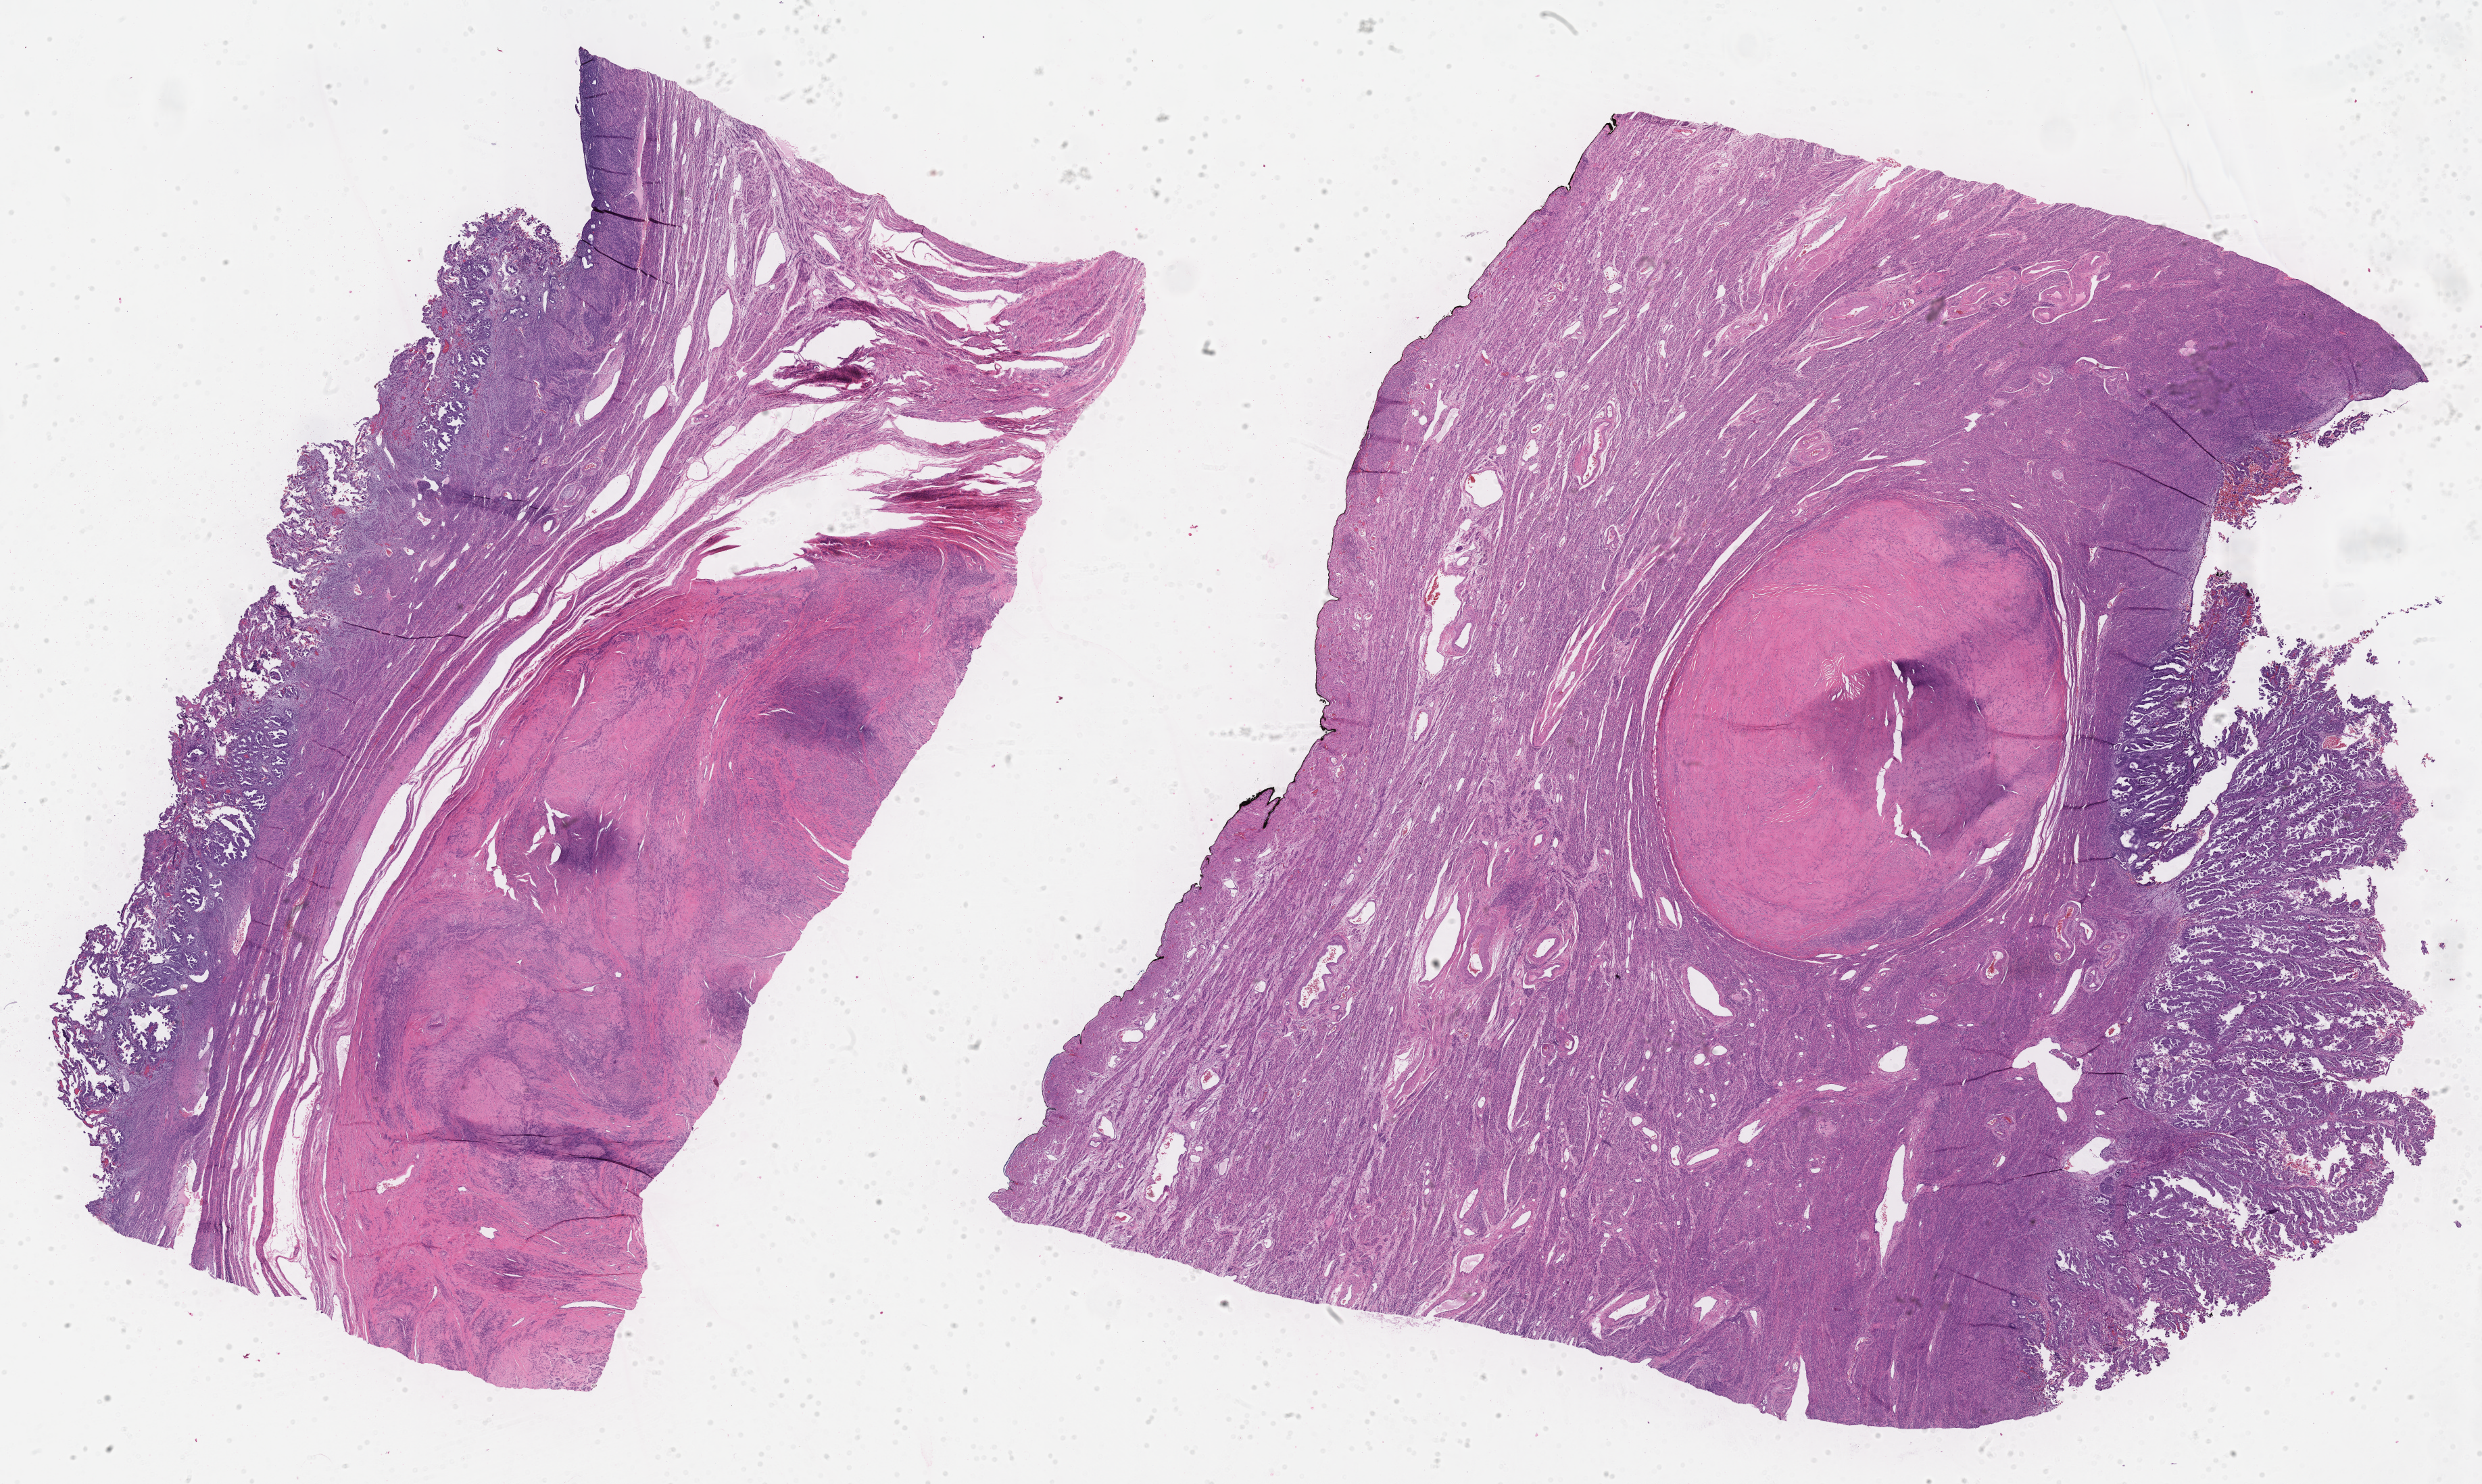
Haematoxylin and eosin whole-slide image, whole scanned area (about 29.6 x 17.7 mm) shown as a low-resolution overview, formalin-fixed paraffin-embedded section, primary tumor, anatomic site: endometrium. Female, age 63 years at initial diagnosis. Pathologist review of this section (percent, as recorded): tumor cells 15%, tumor nuclei 20%, stromal cells 0%, necrosis 0%, normal cells 85%. Inflammatory infiltration, as recorded: lymphocyte infiltration 0%, monocyte infiltration 0%, neutrophil infiltration 0%.
AJCC pathologic stage: Stage I. Section: top of the tissue portion. Histologic diagnosis: Serous carcinoma, NOS.